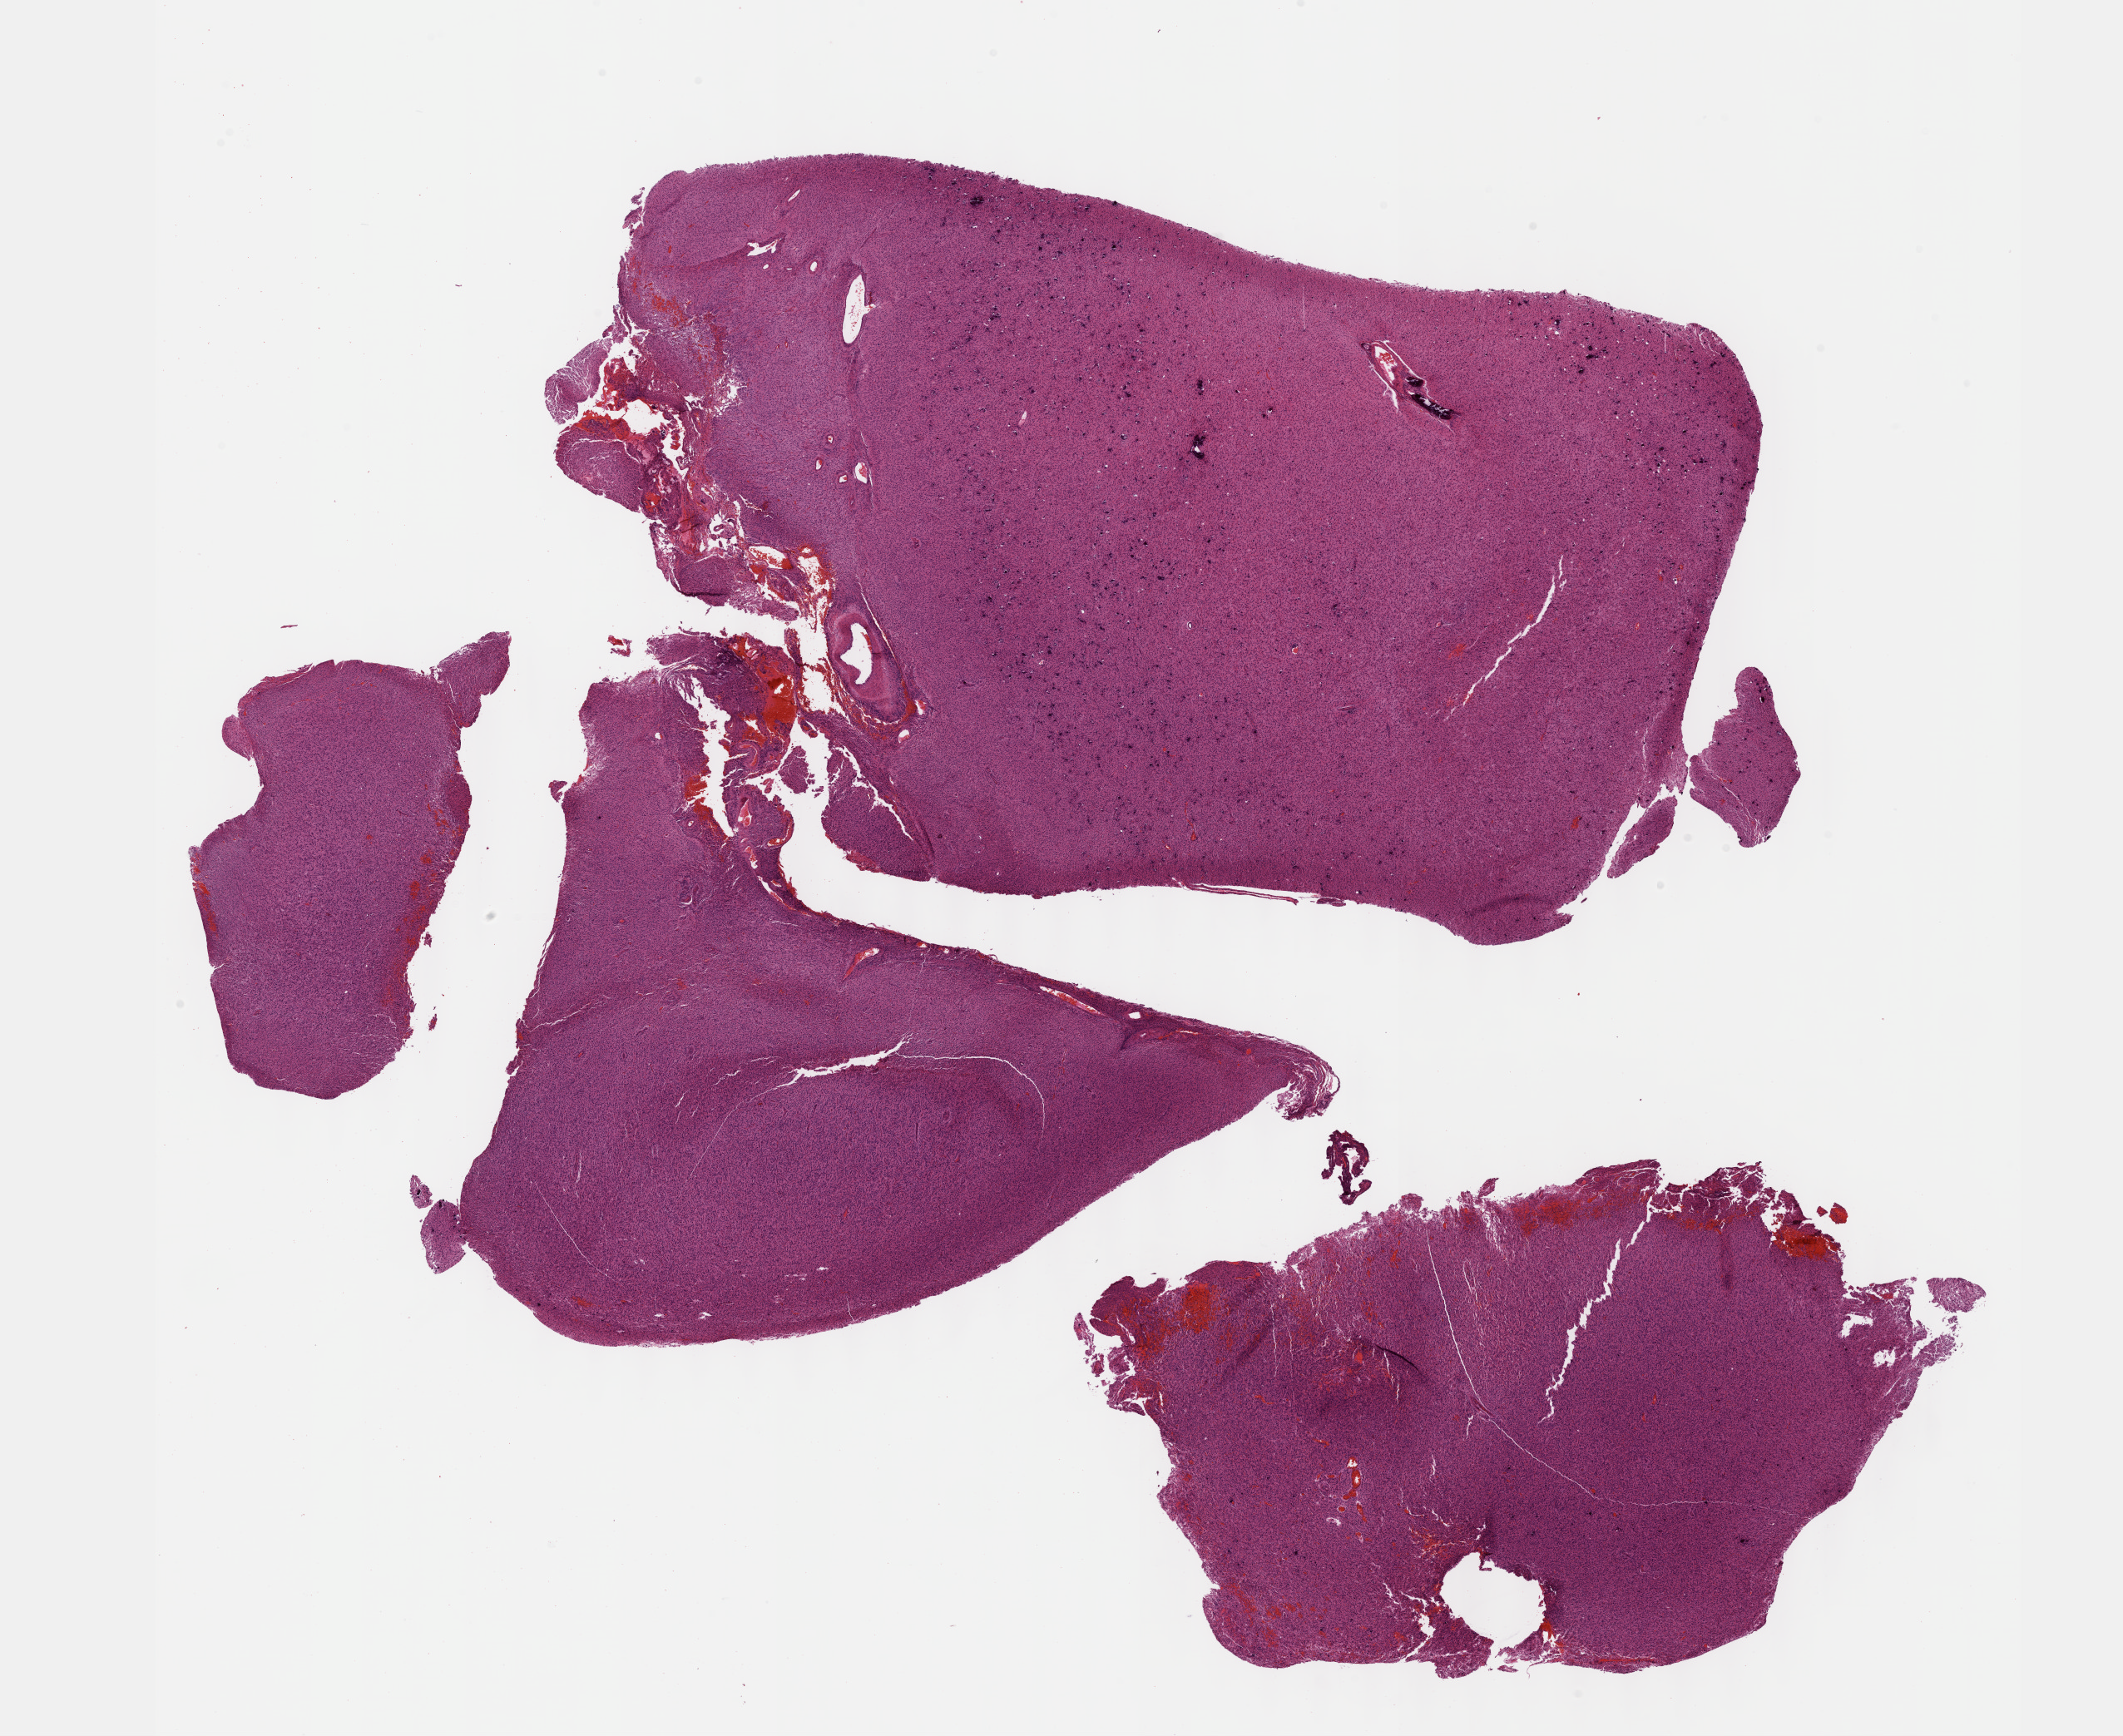
Digitized H&E tissue section (whole slide), low-resolution overview of the scanned area, about 20.6 x 16.9 mm. Formalin-fixed paraffin-embedded (FFPE) diagnostic section. Primary tumour sample from the brain. Female, age 60 years at initial diagnosis. Histologic grade: G3 (poorly differentiated).
Pathologic diagnosis: Astrocytoma, anaplastic (cerebrum). Laterality: left.